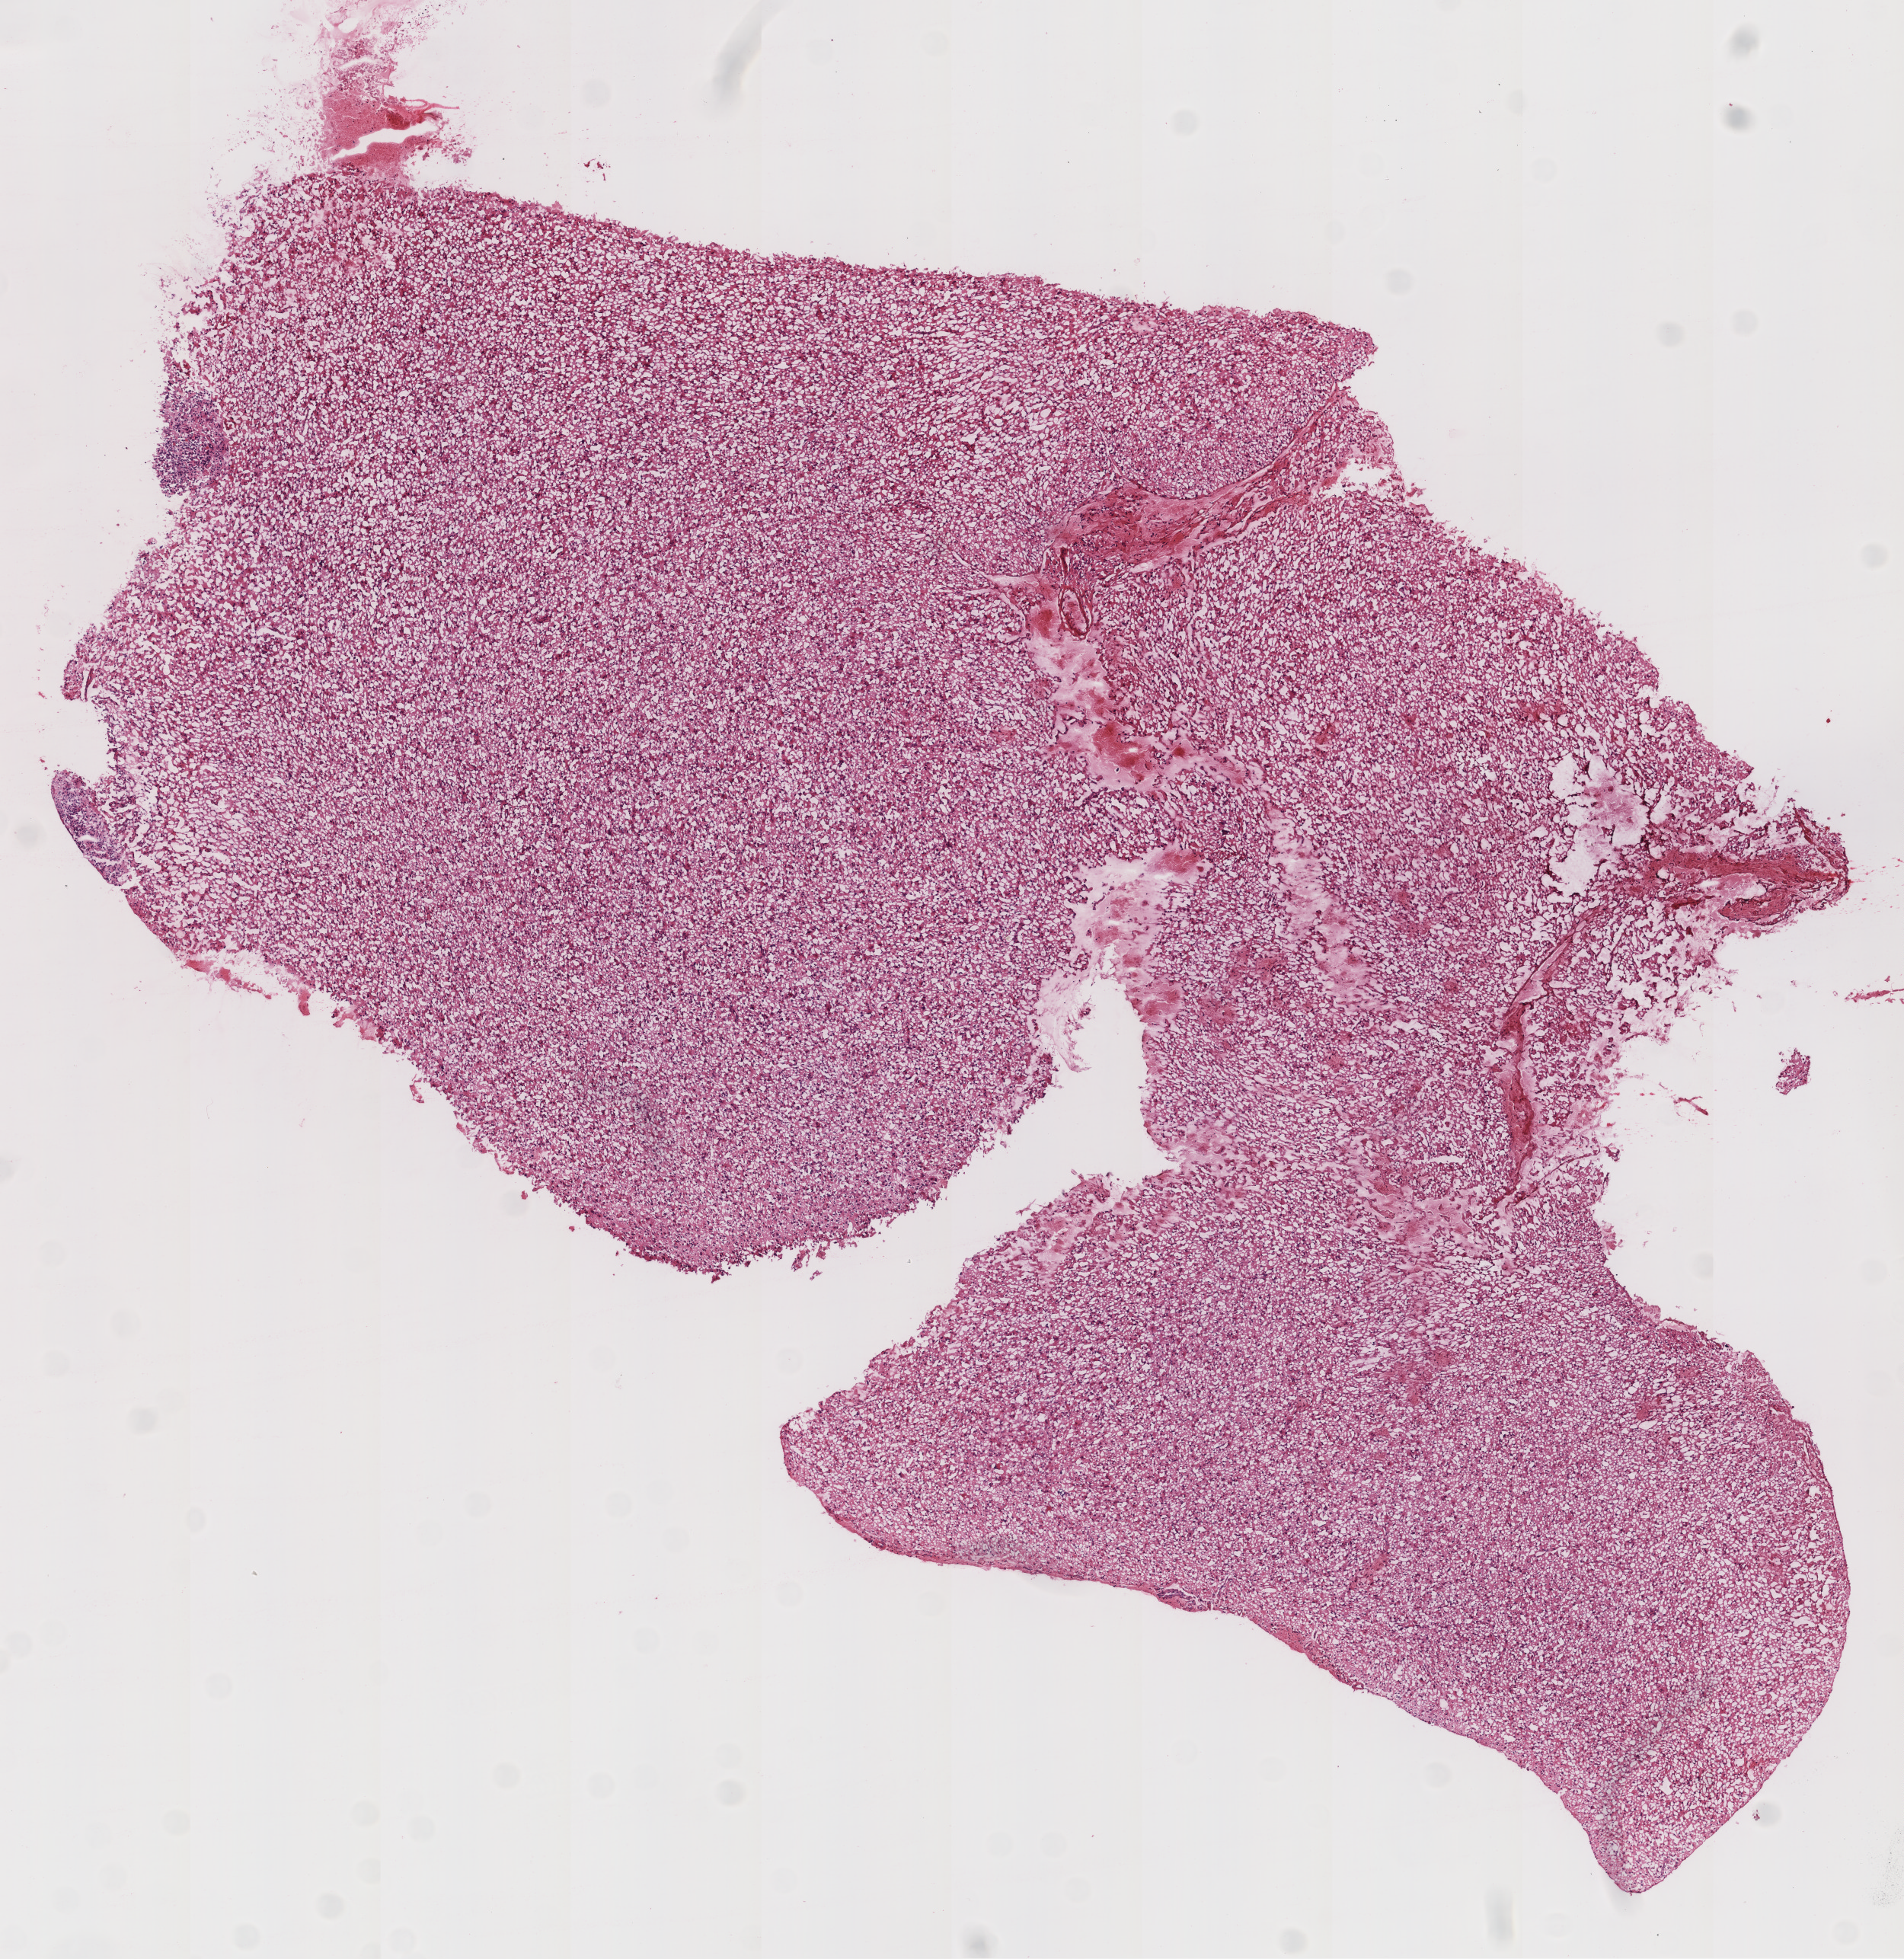
H&E-stained whole-slide image, low-resolution overview of the scanned area, about 10.0 x 10.3 mm (slide scanned at 20x); frozen section from the top of the tissue portion; sample: primary tumour, brain. Patient: male, age at initial diagnosis 76 years. Slide review estimates, as recorded: tumour cells 98%, tumour nuclei 80%.
Pathologic diagnosis: Glioblastoma.